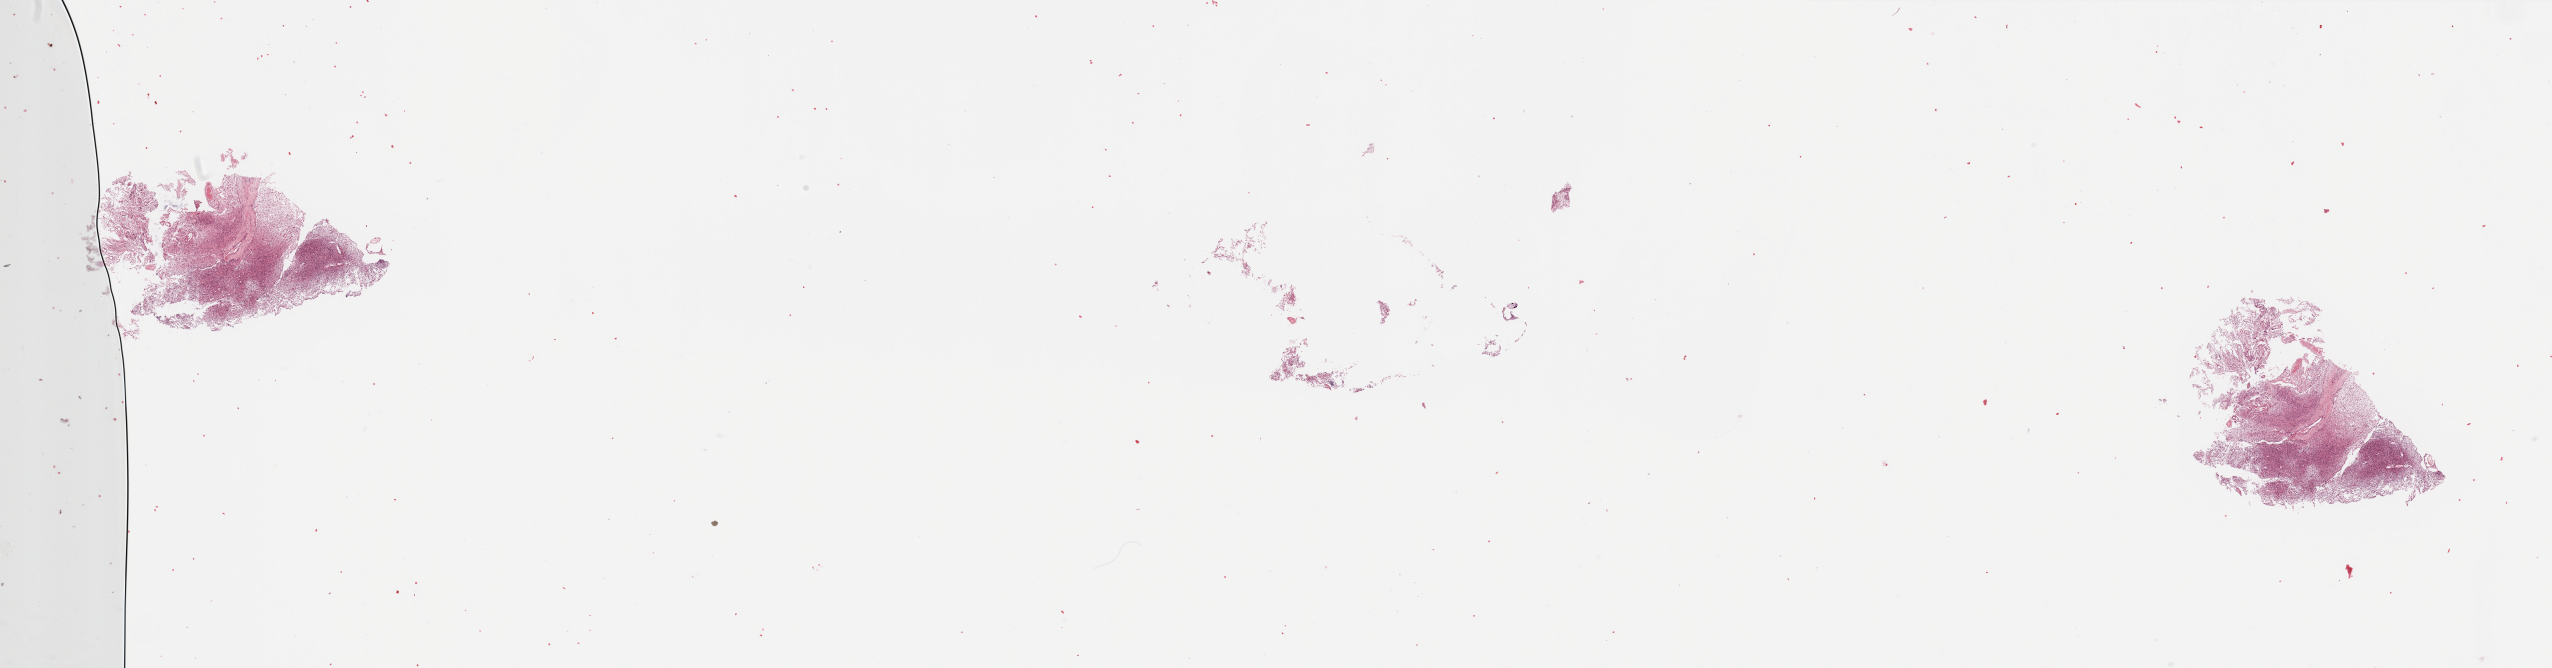
Digitized H&E tissue section (whole slide), low-resolution overview of the scanned area, about 40.4 x 10.6 mm (acquisition: 20x scan), brain, tumour tissue. Patient: male, age 65 years.
* primary tumour site (as recorded): frontal lobe
* diagnosis: Glioblastoma